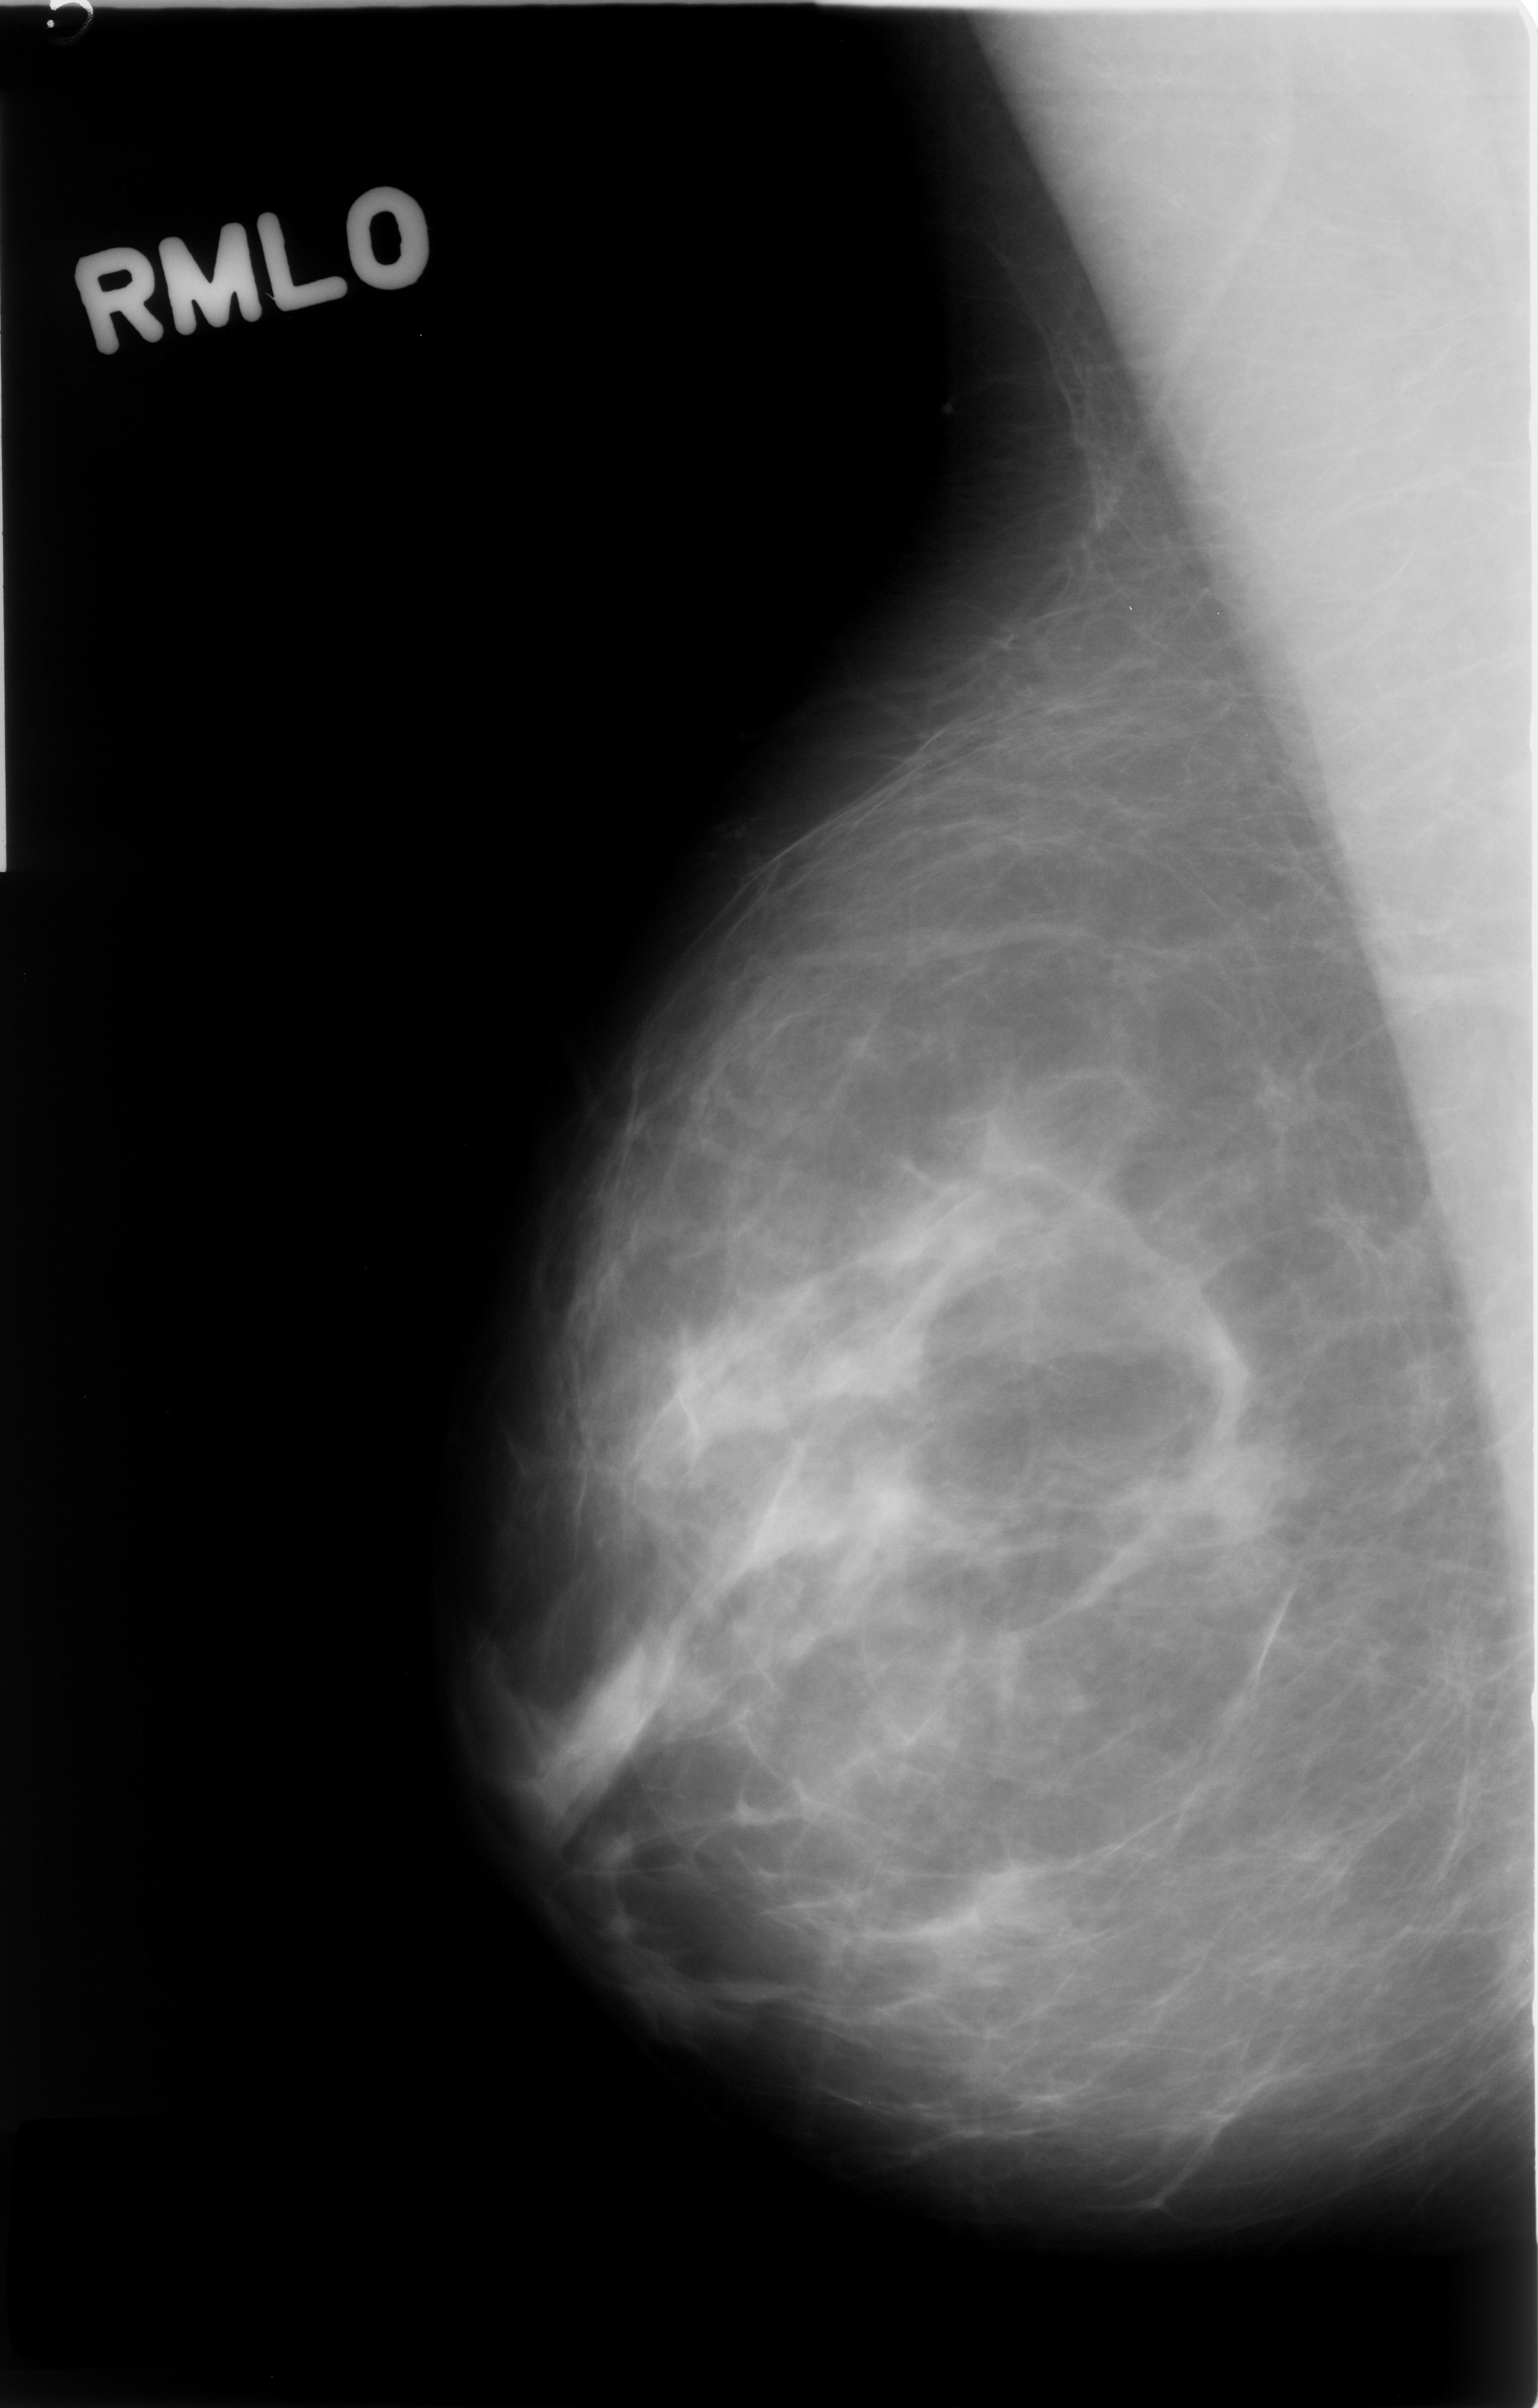
Digitized screen-film mammogram; right breast; mediolateral oblique (MLO) view; breast composition: scattered fibroglandular densities (BI-RADS density category 2 of 4); 1538 × 2408 image matrix.
Expert-marked regions of interest on this image (one box per marked abnormality):
- mass, shape irregular, margins ill defined; BI-RADS assessment category 3; outcome (as recorded, no biopsy): benign without callback (not worked up further): bounding box (x1, y1, x2, y2) in pixels: (1114, 1358, 1307, 1573)